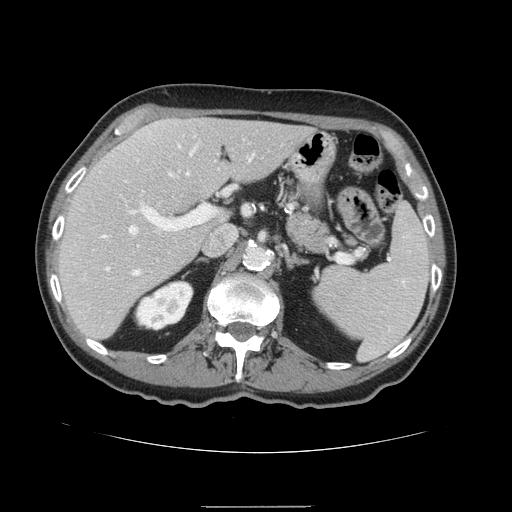
Contrast-enhanced abdominal CT, one axial slice; slice 93 of 168 in the series (ordered by position); 120 kVp; intravenous contrast given; soft-tissue window (W 400 / L 40 HU); 2.5 mm slice thickness; 512 × 512 image matrix, field of view 386 × 386 mm. Male patient, age 74 years. From the clinical record (not read from this slice): diagnosis: colorectal cancer liver metastases, imaged before liver resection.
Structures marked on this image (manually delineated by an expert):
- hepatic veins: bounding box <129,151,252,274> (left, top, right, bottom; pixels)
- liver: <58,119,314,341>
- planned liver remnant (the part of the liver to remain after resection): <58,119,315,340>
- portal vein (with intrahepatic branches): <99,195,215,271>